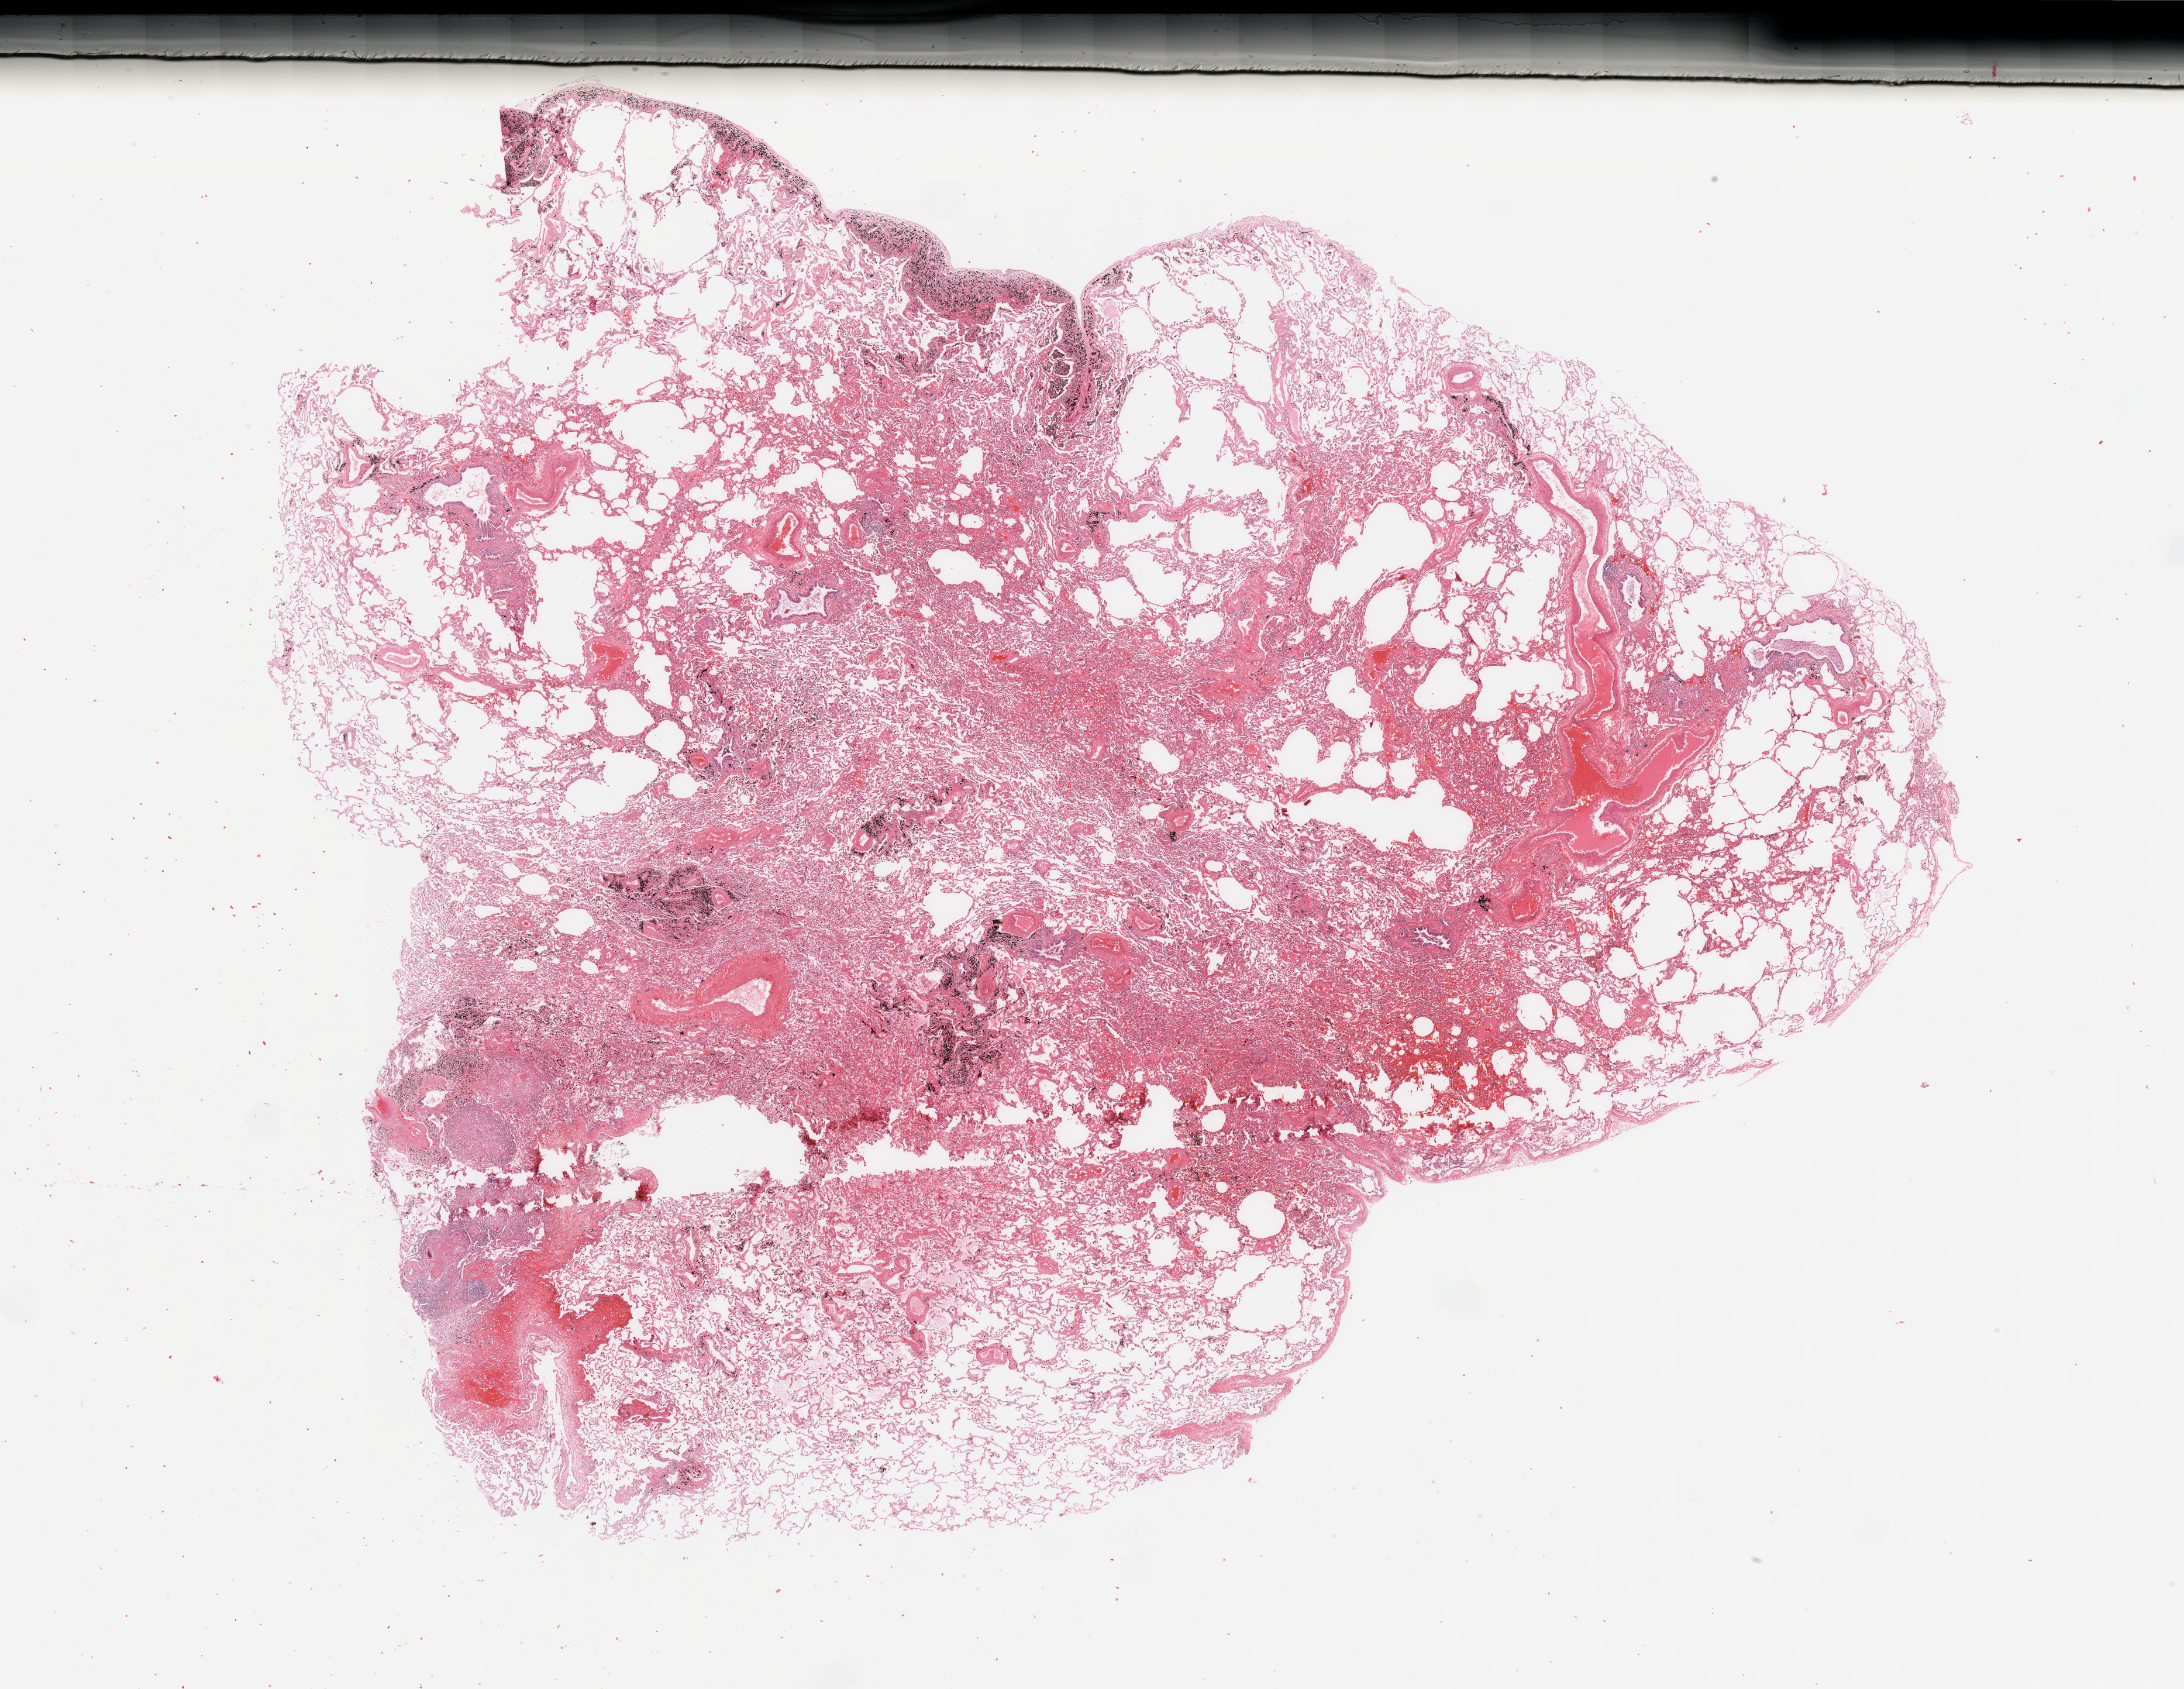
Digitized Hematoxylin and eosin (H&E) stained tissue section (whole slide), whole scanned area (about 29.5 x 22.8 mm, slide scanned at 20x) shown as a low-resolution overview, normal (non-tumour) tissue sample, lung. Male, 64 y/o.
* this section: normal (non-tumour) tissue from the same patient
* patient diagnosis: Adenocarcinoma, NOS